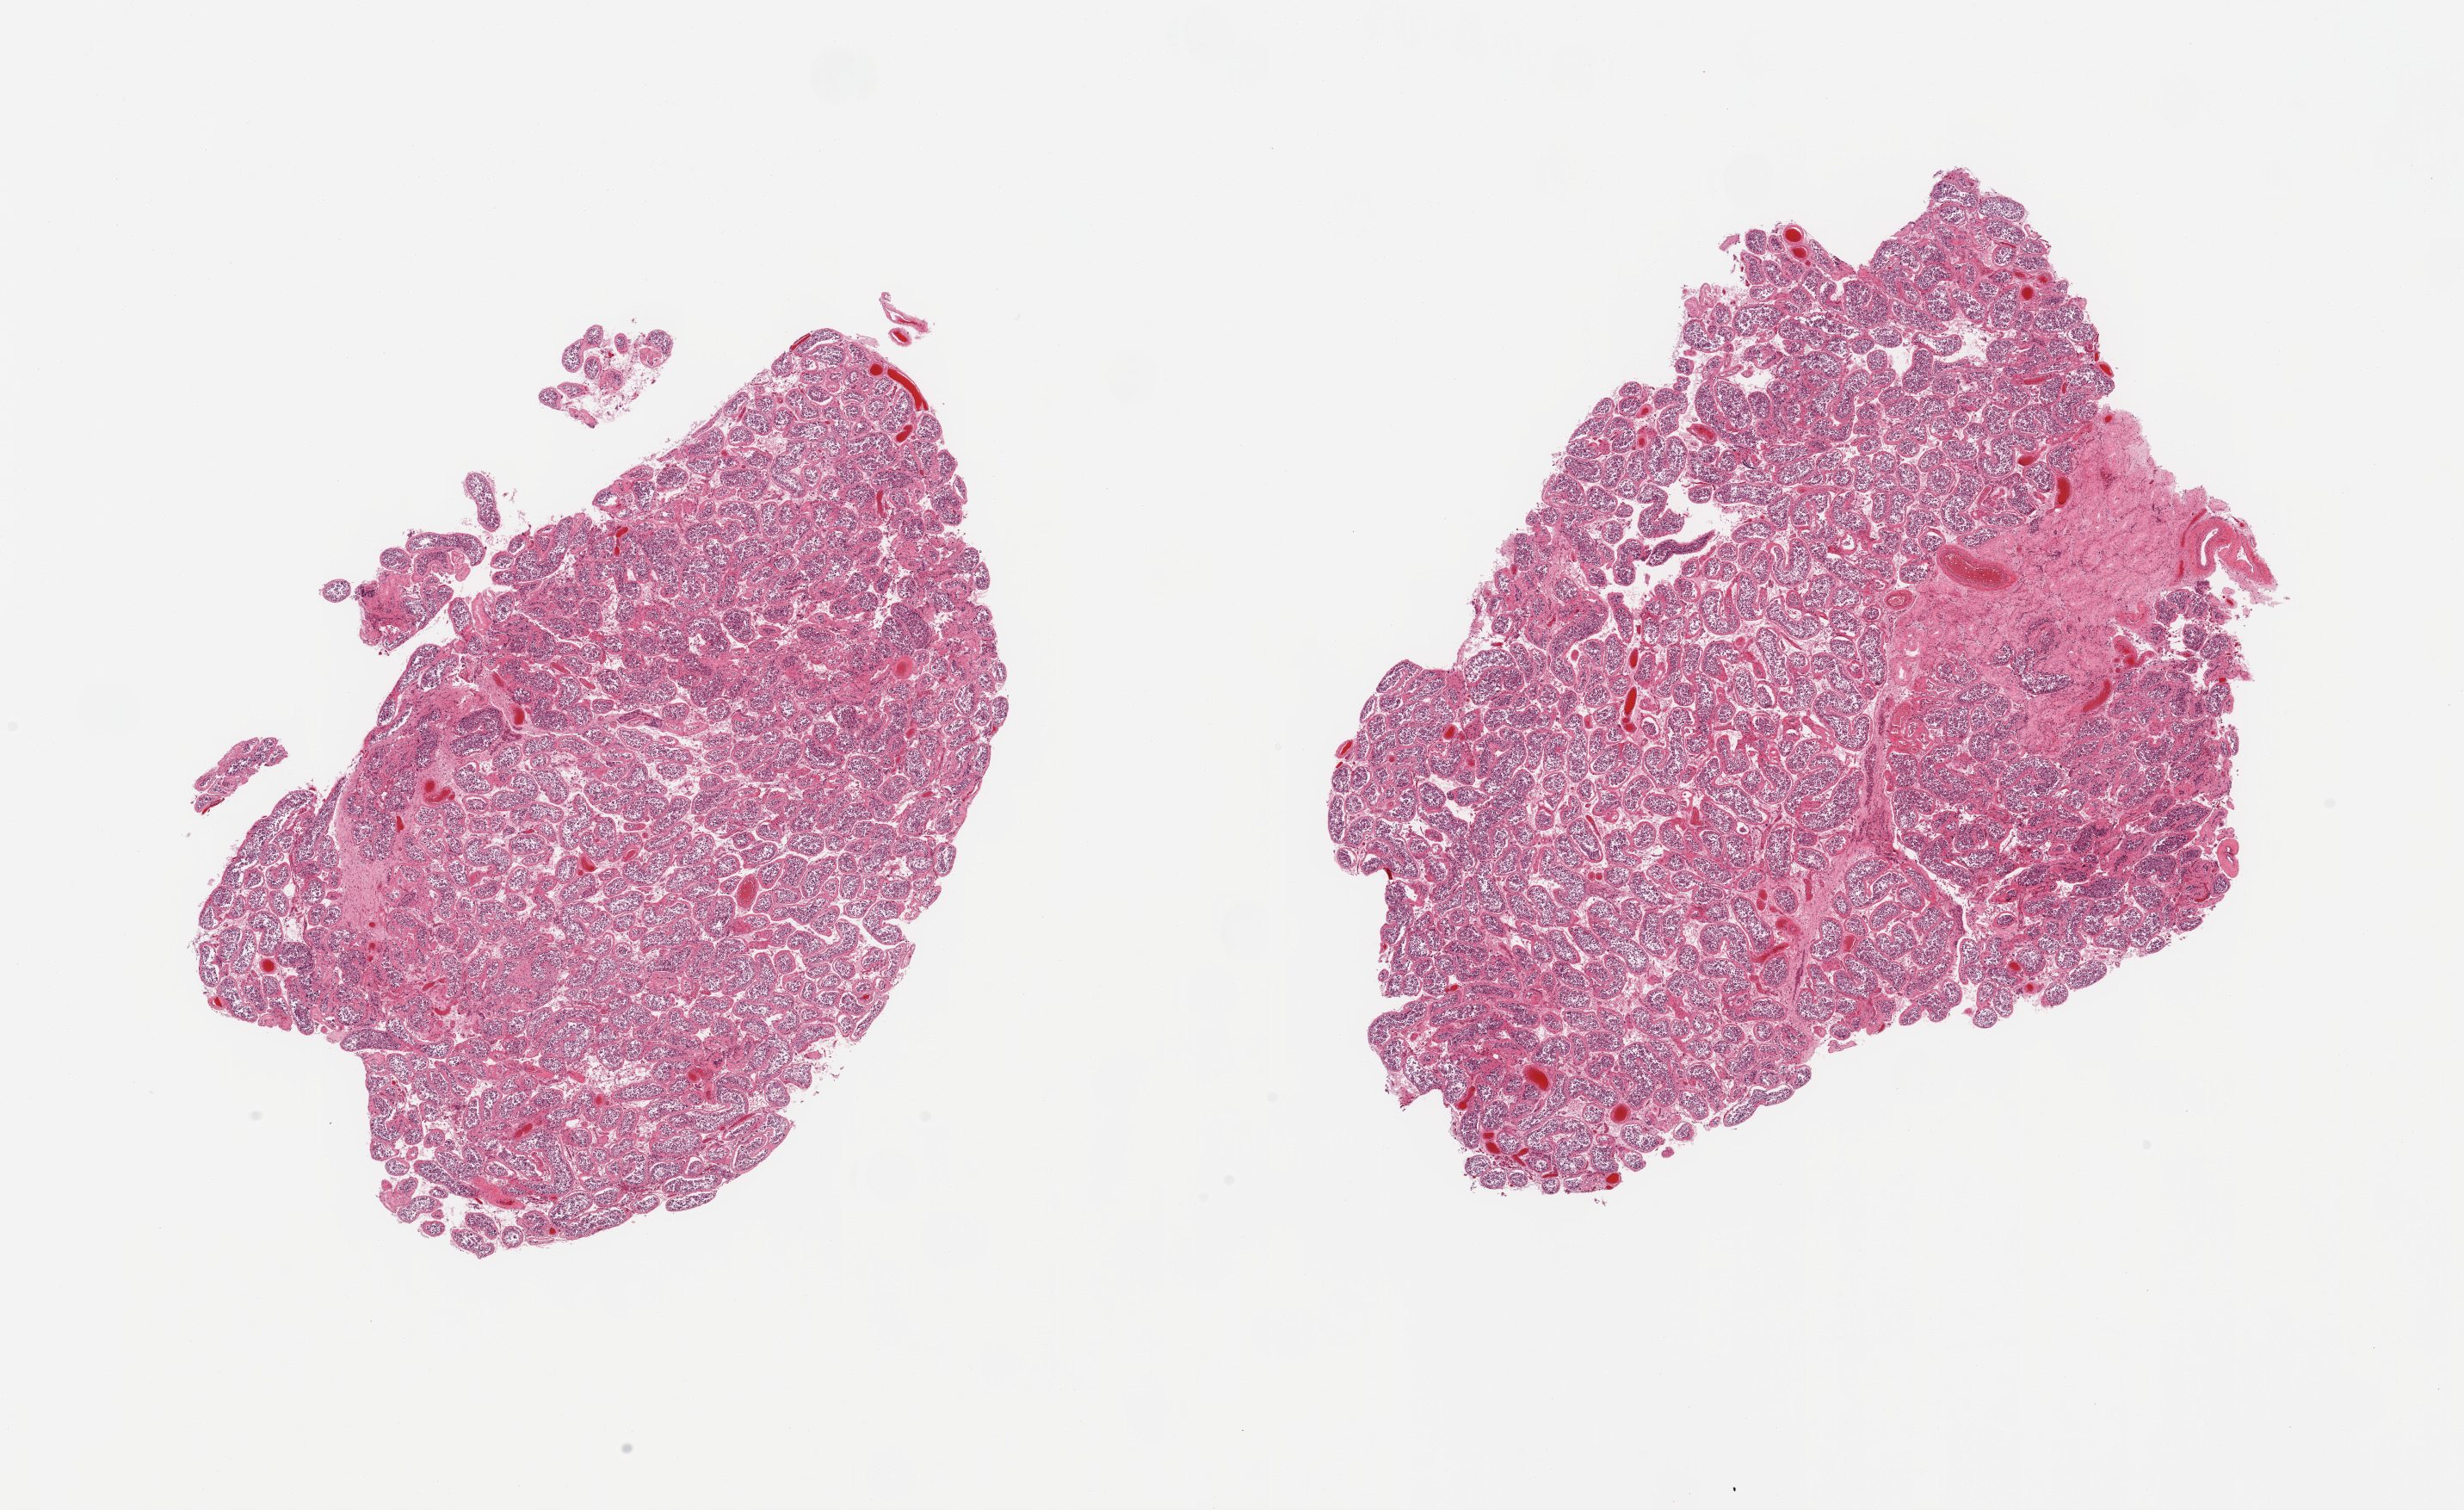
H&E whole-slide image — shown as a low-resolution overview of the whole scanned area (about 22.6 x 13.9 mm, acquisition: 20x scan); PAXgene-fixed, paraffin-embedded tissue; sampled site (target tissue): testis; donor tissue sample. Donor: male.
• pathologist's review note for this sample: 2 pieces, spermatogenesis appears markedly reduced